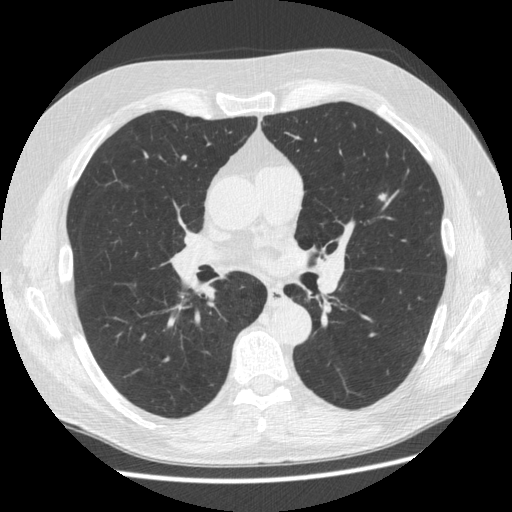
Low-dose screening chest CT, one axial slice. Slice 302 of 545 in the series (ordered by position). 120 kVp. Lung window (W 1500 / L -600 HU). 1.25 mm slice thickness. 512 × 512 image matrix, field of view 360 × 360 mm.
Outlined on this slice (expert manual segmentation):
- lesion 1 (nodule, upper lobe of left lung): box from (x=378, y=193) to (x=386, y=202) px